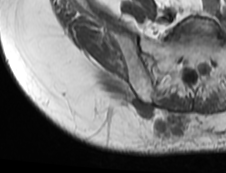
MRI of an extremity soft-tissue mass, one axial slice; slice 55 of 73 in the series (ordered by position); MR volume resampled by the dataset authors to the PET/CT grid (not the native acquisition matrix); 3.27 mm slice thickness; 226 × 173 image matrix. Female patient. Case-level facts recorded for this patient, not image findings: histological type: spindle cell suggestive of myxofibrosarcoma; grade: intermediate; site of the primary tumour: right buttock.
Outlined on this slice (expert contour drawn on MRI and transferred to this co-registered scan by the dataset authors):
- gross tumour volume (mass): bounding box (x1, y1, x2, y2) in pixels: (116, 95, 185, 139)